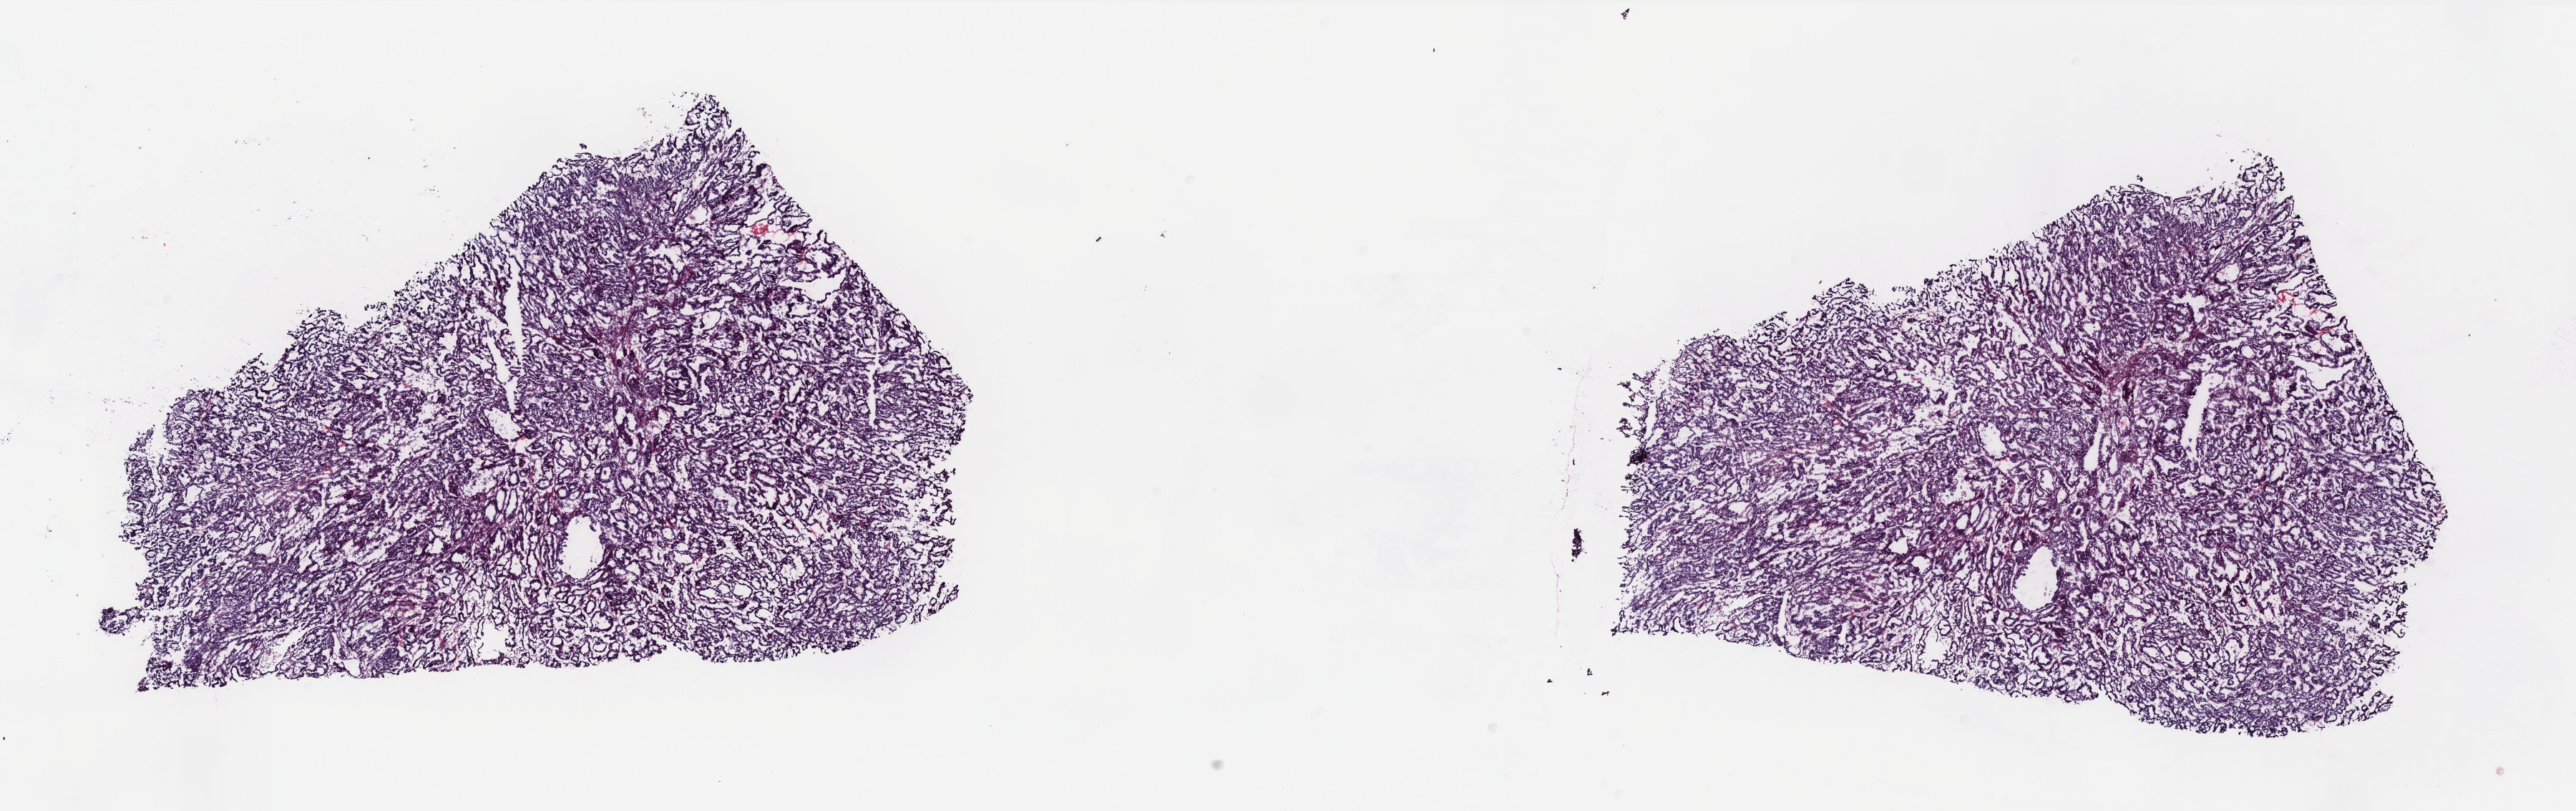
Digitized H&E-stained tissue section (whole slide), low-resolution overview of the scanned area, about 28.9 x 9.1 mm, frozen section, primary tumour sample from the uterus. Female, age 66 years at initial diagnosis. Histologic grade: G1 (well differentiated). Pathologist review of this section (percent, as recorded): tumour cells 100%, tumour nuclei 95%, normal cells 0%, stromal cells 0%, necrosis 0%. Inflammatory infiltration, as recorded: lymphocyte infiltration 0%, monocyte infiltration 2%, neutrophil infiltration 2%.
• diagnosis: Endometrioid adenocarcinoma, NOS (endometrium)
• FIGO stage: IA